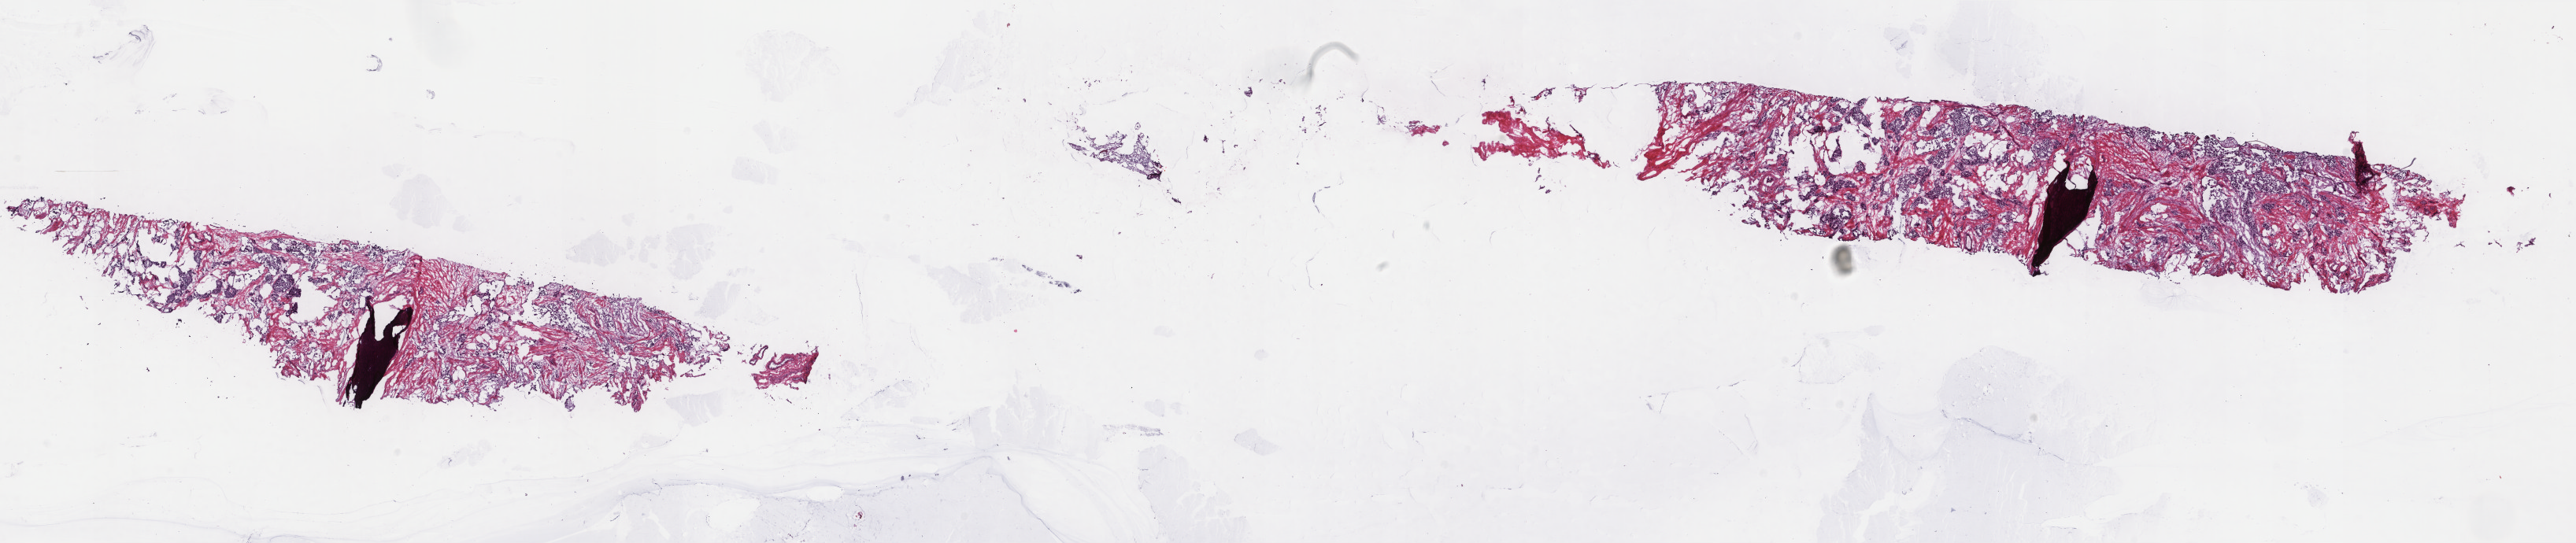
Whole-slide histology image, Hematoxylin and eosin (H&E) stained, low-resolution overview of the scanned area, about 26.0 x 5.5 mm (slide scanned at 40x). Frozen section from the top of the tissue portion. Breast, primary tumour sample. Female patient; age at initial diagnosis 63 years. Pathologist review of this section (percent, as recorded): tumour cells 80%, tumour nuclei 80%, normal cells 0%, stromal cells 18%, necrosis 2%. Inflammatory infiltration, as recorded: lymphocyte infiltration 2%, monocyte infiltration 1%, neutrophil infiltration 1%.
* lymph nodes positive (case pathology): 0 of 1 examined
* pathologic diagnosis: Infiltrating duct carcinoma, NOS
* AJCC pathologic stage: I (6th edition)
* TNM: T1c N0 M0